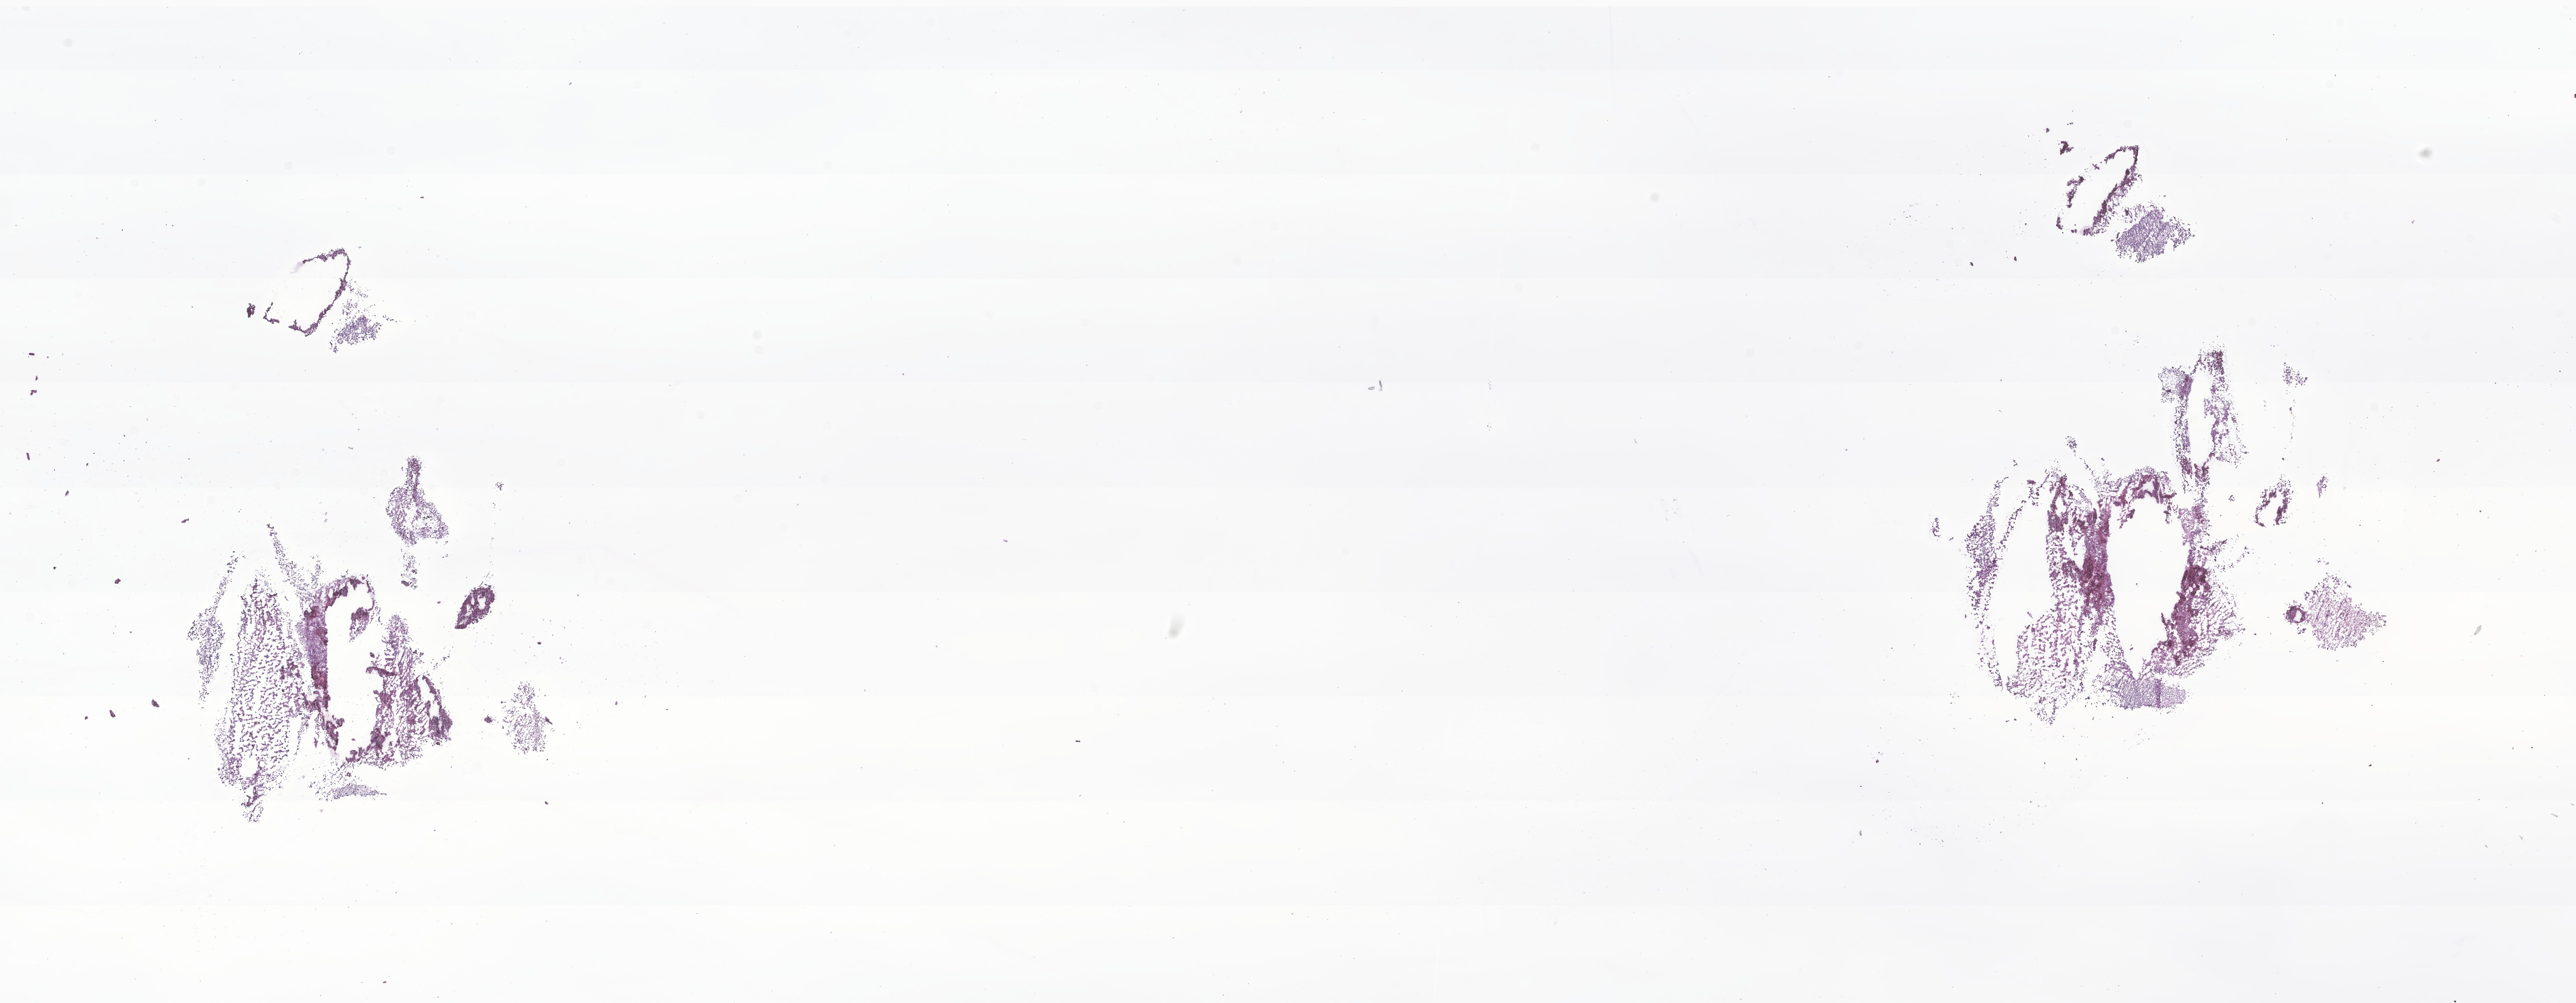
Digitized hematoxylin and eosin (H&E)-stained section of tumor tissue from the eye — a low-resolution overview of the entire scanned area, about 26.3 x 10.3 mm; frozen section (OCT-embedded). Male patient, age 372 days (about 1.0 years).
Diagnosis: Neoplasm, uncertain whether benign or malignant.